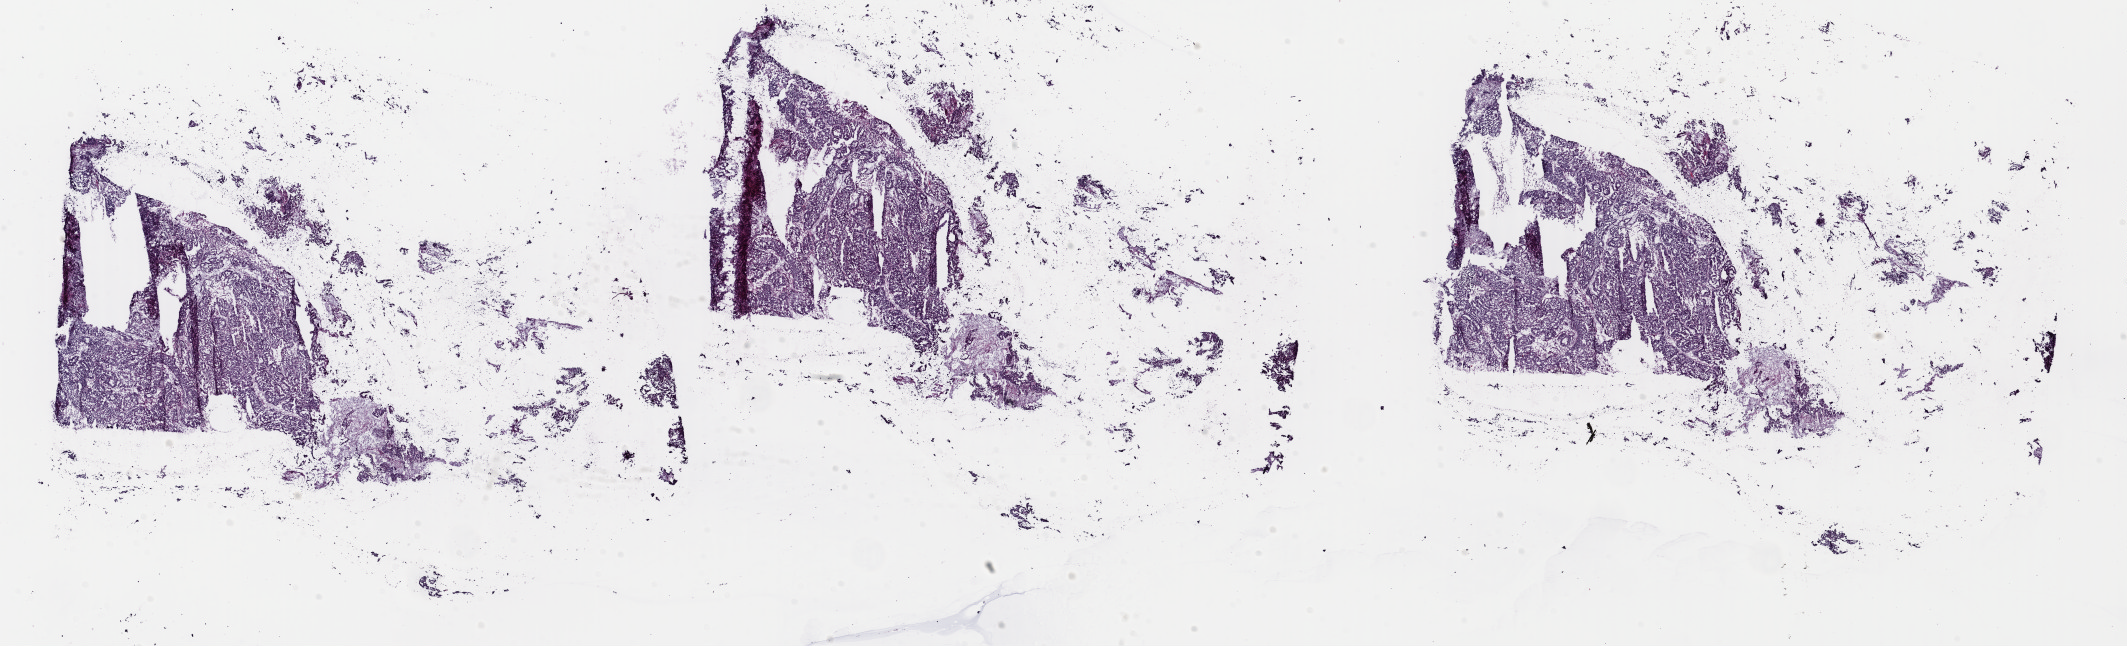
Digitized Hematoxylin and eosin (H&E) stained tissue section (whole slide) — whole scanned area (about 33.4 x 10.2 mm) shown as a low-resolution overview. Frozen section from the top of the tissue portion. Sample: primary tumour, uterus. Female patient. Histologic grade: G3 (poorly differentiated). Slide review estimates, as recorded: tumour cells 90%, tumour nuclei 90%, normal cells 0%, stromal cells 8%, necrosis 2%. Infiltration values recorded for this section: lymphocyte infiltration 0%, monocyte infiltration 0%, neutrophil infiltration 0%.
Diagnosis: Serous cystadenocarcinoma, NOS (endometrium). FIGO stage: IA. Lymph nodes positive (case pathology): 0 of 16 examined.